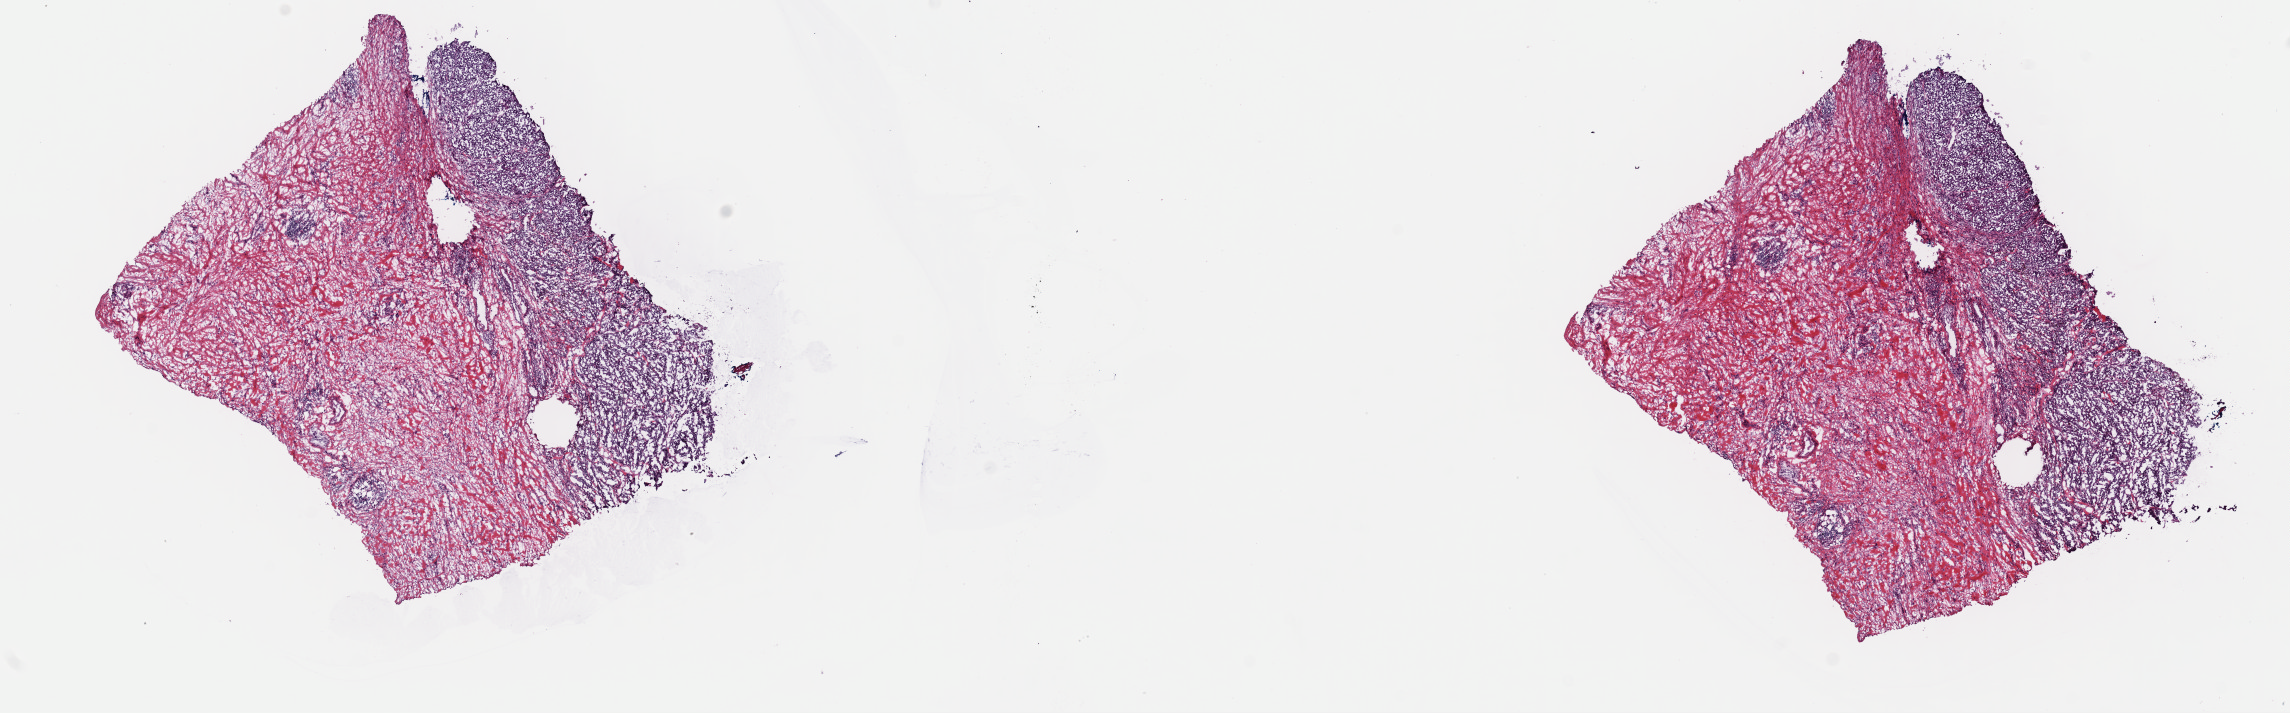
H&E-stained whole-slide image — whole scanned area (about 18.1 x 5.6 mm) shown as a low-resolution overview. Frozen section. Metastatic tumour sample. Patient: male, age at initial diagnosis 20 years. Pathologist review of this section (percent, as recorded): tumour cells 60%, tumour nuclei 60%, normal cells 0%, stromal cells 40%, necrosis 0%. Inflammatory infiltration, as recorded: lymphocyte infiltration 10%, monocyte infiltration 1%, neutrophil infiltration 1%.
This section: metastatic tumour tissue. Patient diagnosis: Malignant melanoma, NOS.